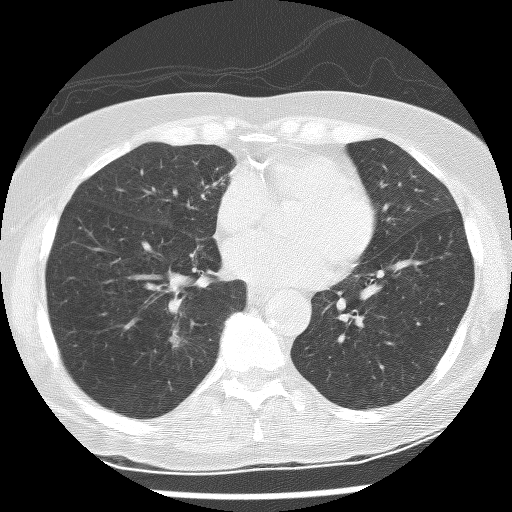
Low-dose screening chest CT, one axial slice. Position 104 of 247 along the scan axis. 120 kVp. Lung window (W 1500 / L -600 HU). 2.5 mm slice thickness. 512 × 512 image matrix.
Structures marked on this image (outlined manually by an expert reader):
- lesion 1 (tumor, lower lobe of right lung): bounding box (x1, y1, x2, y2) in pixels: (169, 328, 186, 348)